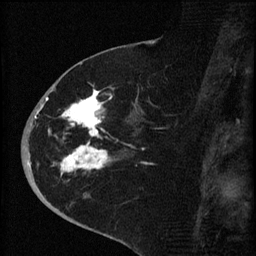
Breast MRI (dynamic contrast-enhanced), one sagittal slice. Slice 30 of 60 in the series (ordered by position). Dynamic contrast-enhanced series, image 2 of 4 at this slice position (ordered by acquisition). 1.5 T. TE 4.2 ms, TR 8.2 ms. 2 mm slice thickness. 256 × 256 image matrix. Female patient, age 71 years.
Annotated regions visible in this slice (semi-automatic segmentation, software-assisted and operator-edited):
- analysis volume of interest (the breast-tissue region the enhancement analysis was run in; not a lesion): bounding box [x1, y1, x2, y2] px = [35, 75, 153, 190]
- tumour enhancement mask (voxels above the 70 % enhancement threshold inside the analysis volume of interest): [35, 85, 112, 176]